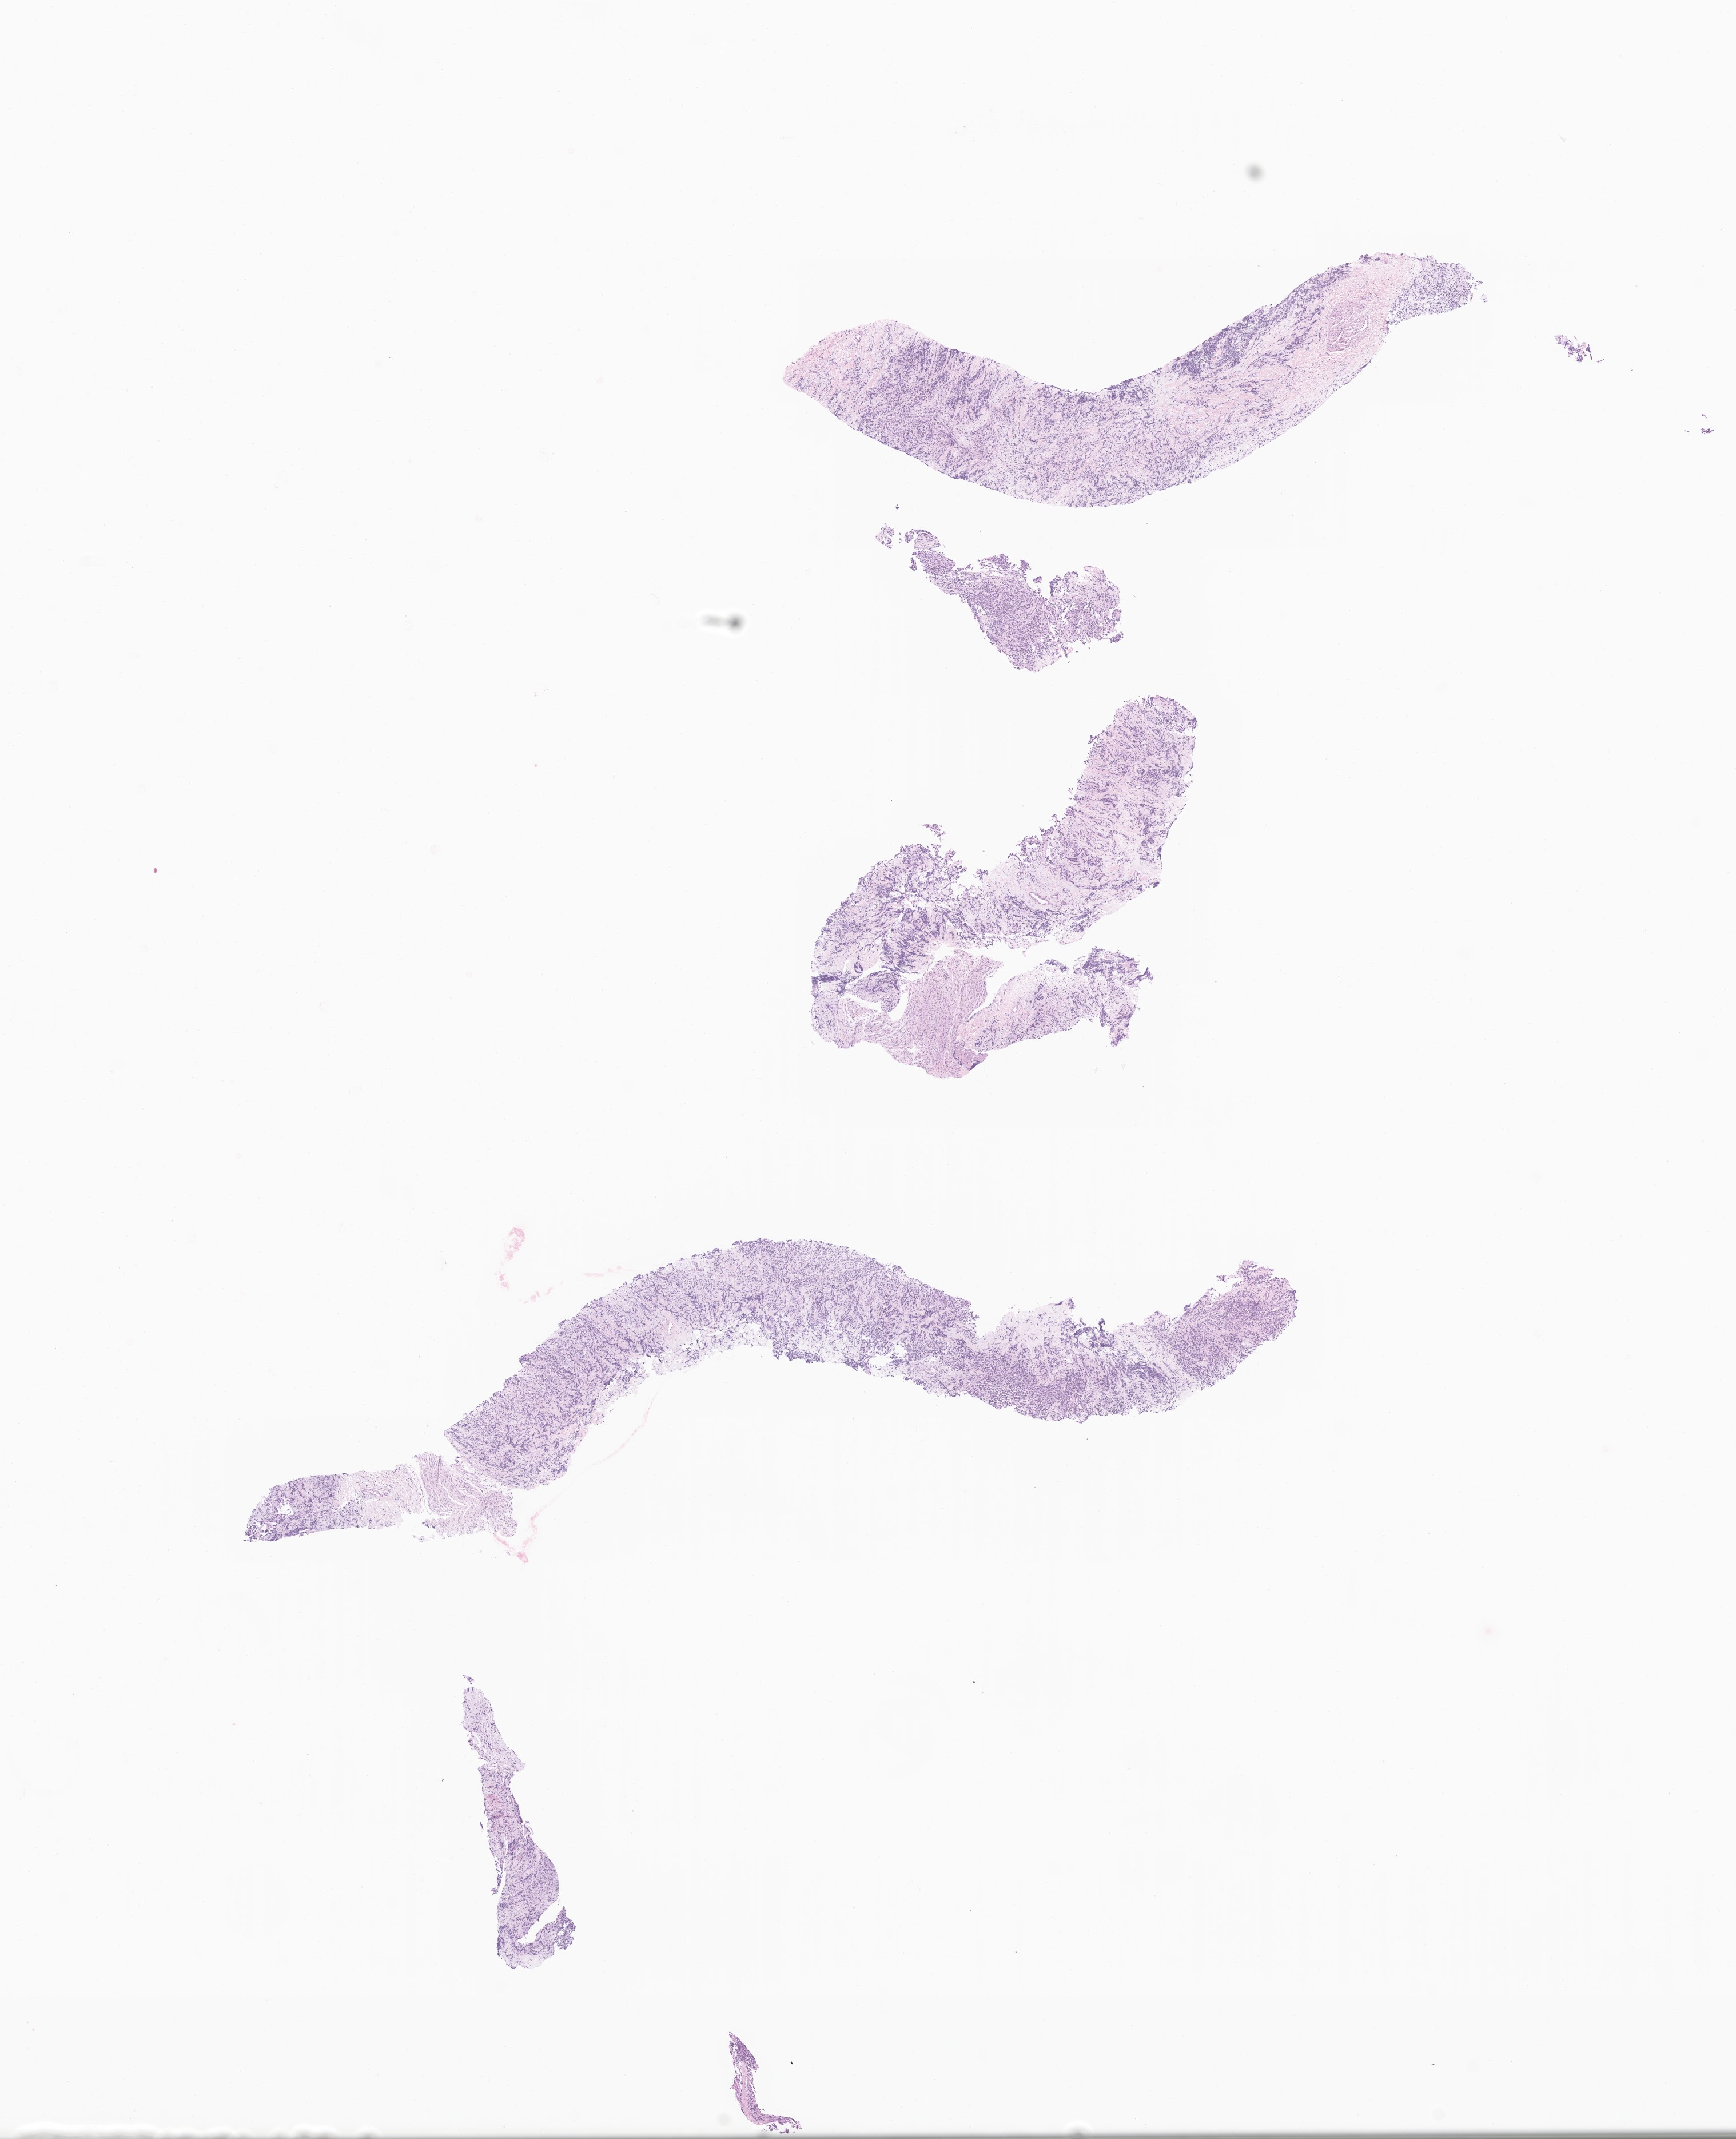
Whole-slide image, hematoxylin and eosin (H&E) stain of tumor tissue from the retroperitoneum, shown as a low-resolution overview of the whole scanned area (about 12.8 x 15.8 mm). Formalin-fixed, paraffin-embedded (FFPE) tissue. Patient male; age 998 days (about 2.7 years).
Diagnosis (ICD-O-3 morphology term): Neuroblastoma, NOS.